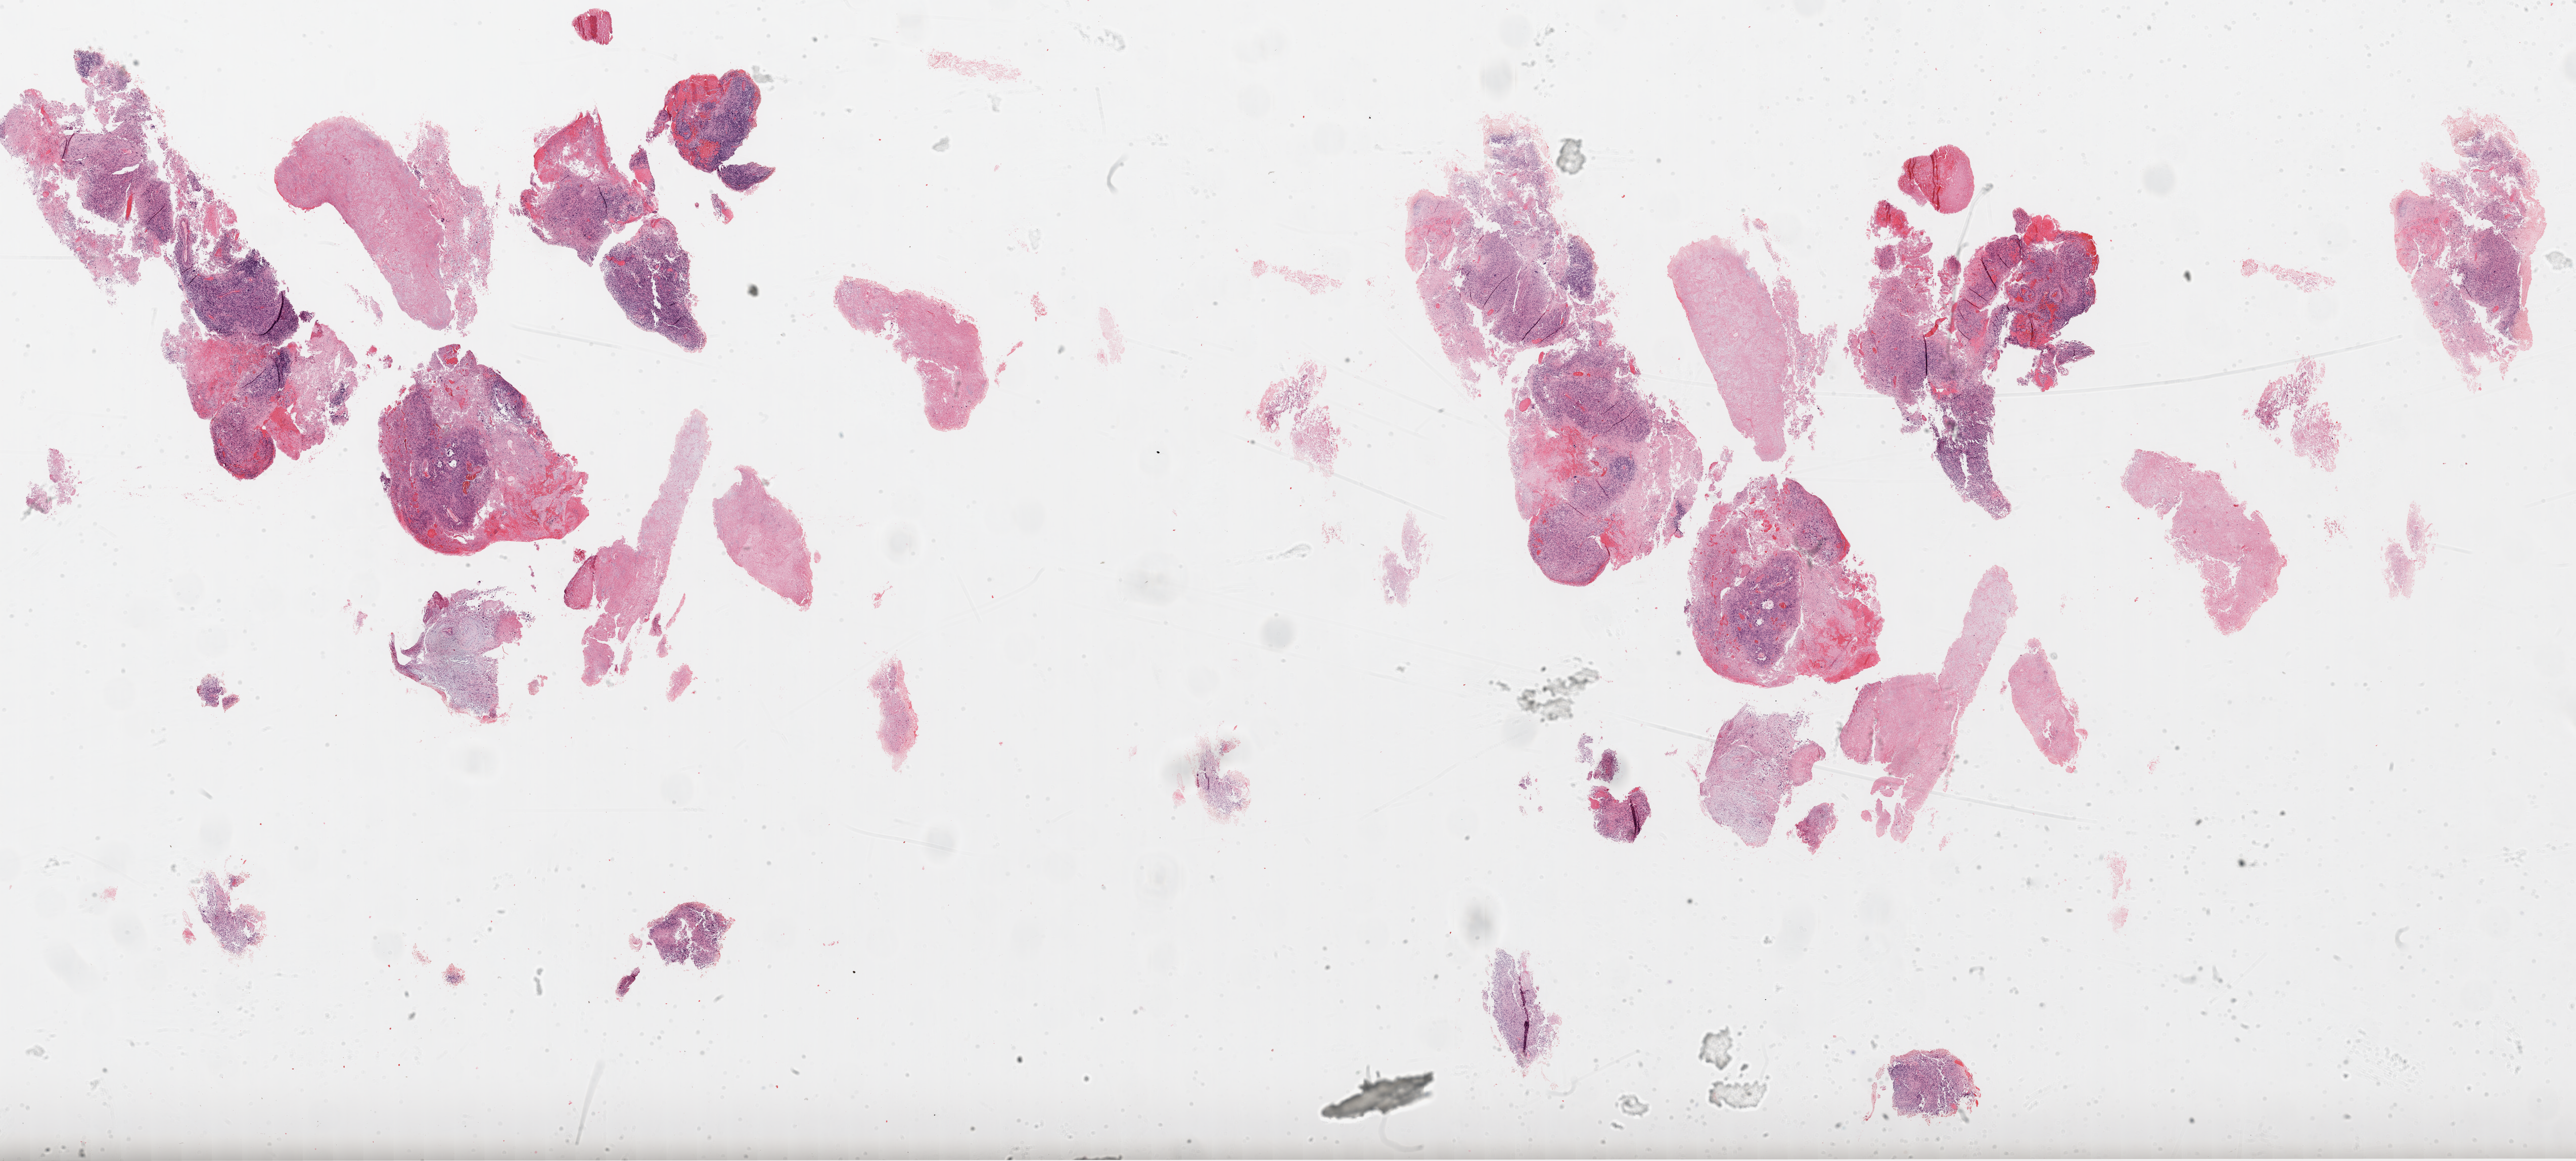
Whole-slide histology image, H&E, low-resolution overview of the scanned area, about 41.1 x 18.5 mm (from a 20x scan); formalin-fixed paraffin-embedded (FFPE) diagnostic section; brain, primary tumour sample. Male patient; age at initial diagnosis 67 years.
- diagnosis: Glioblastoma